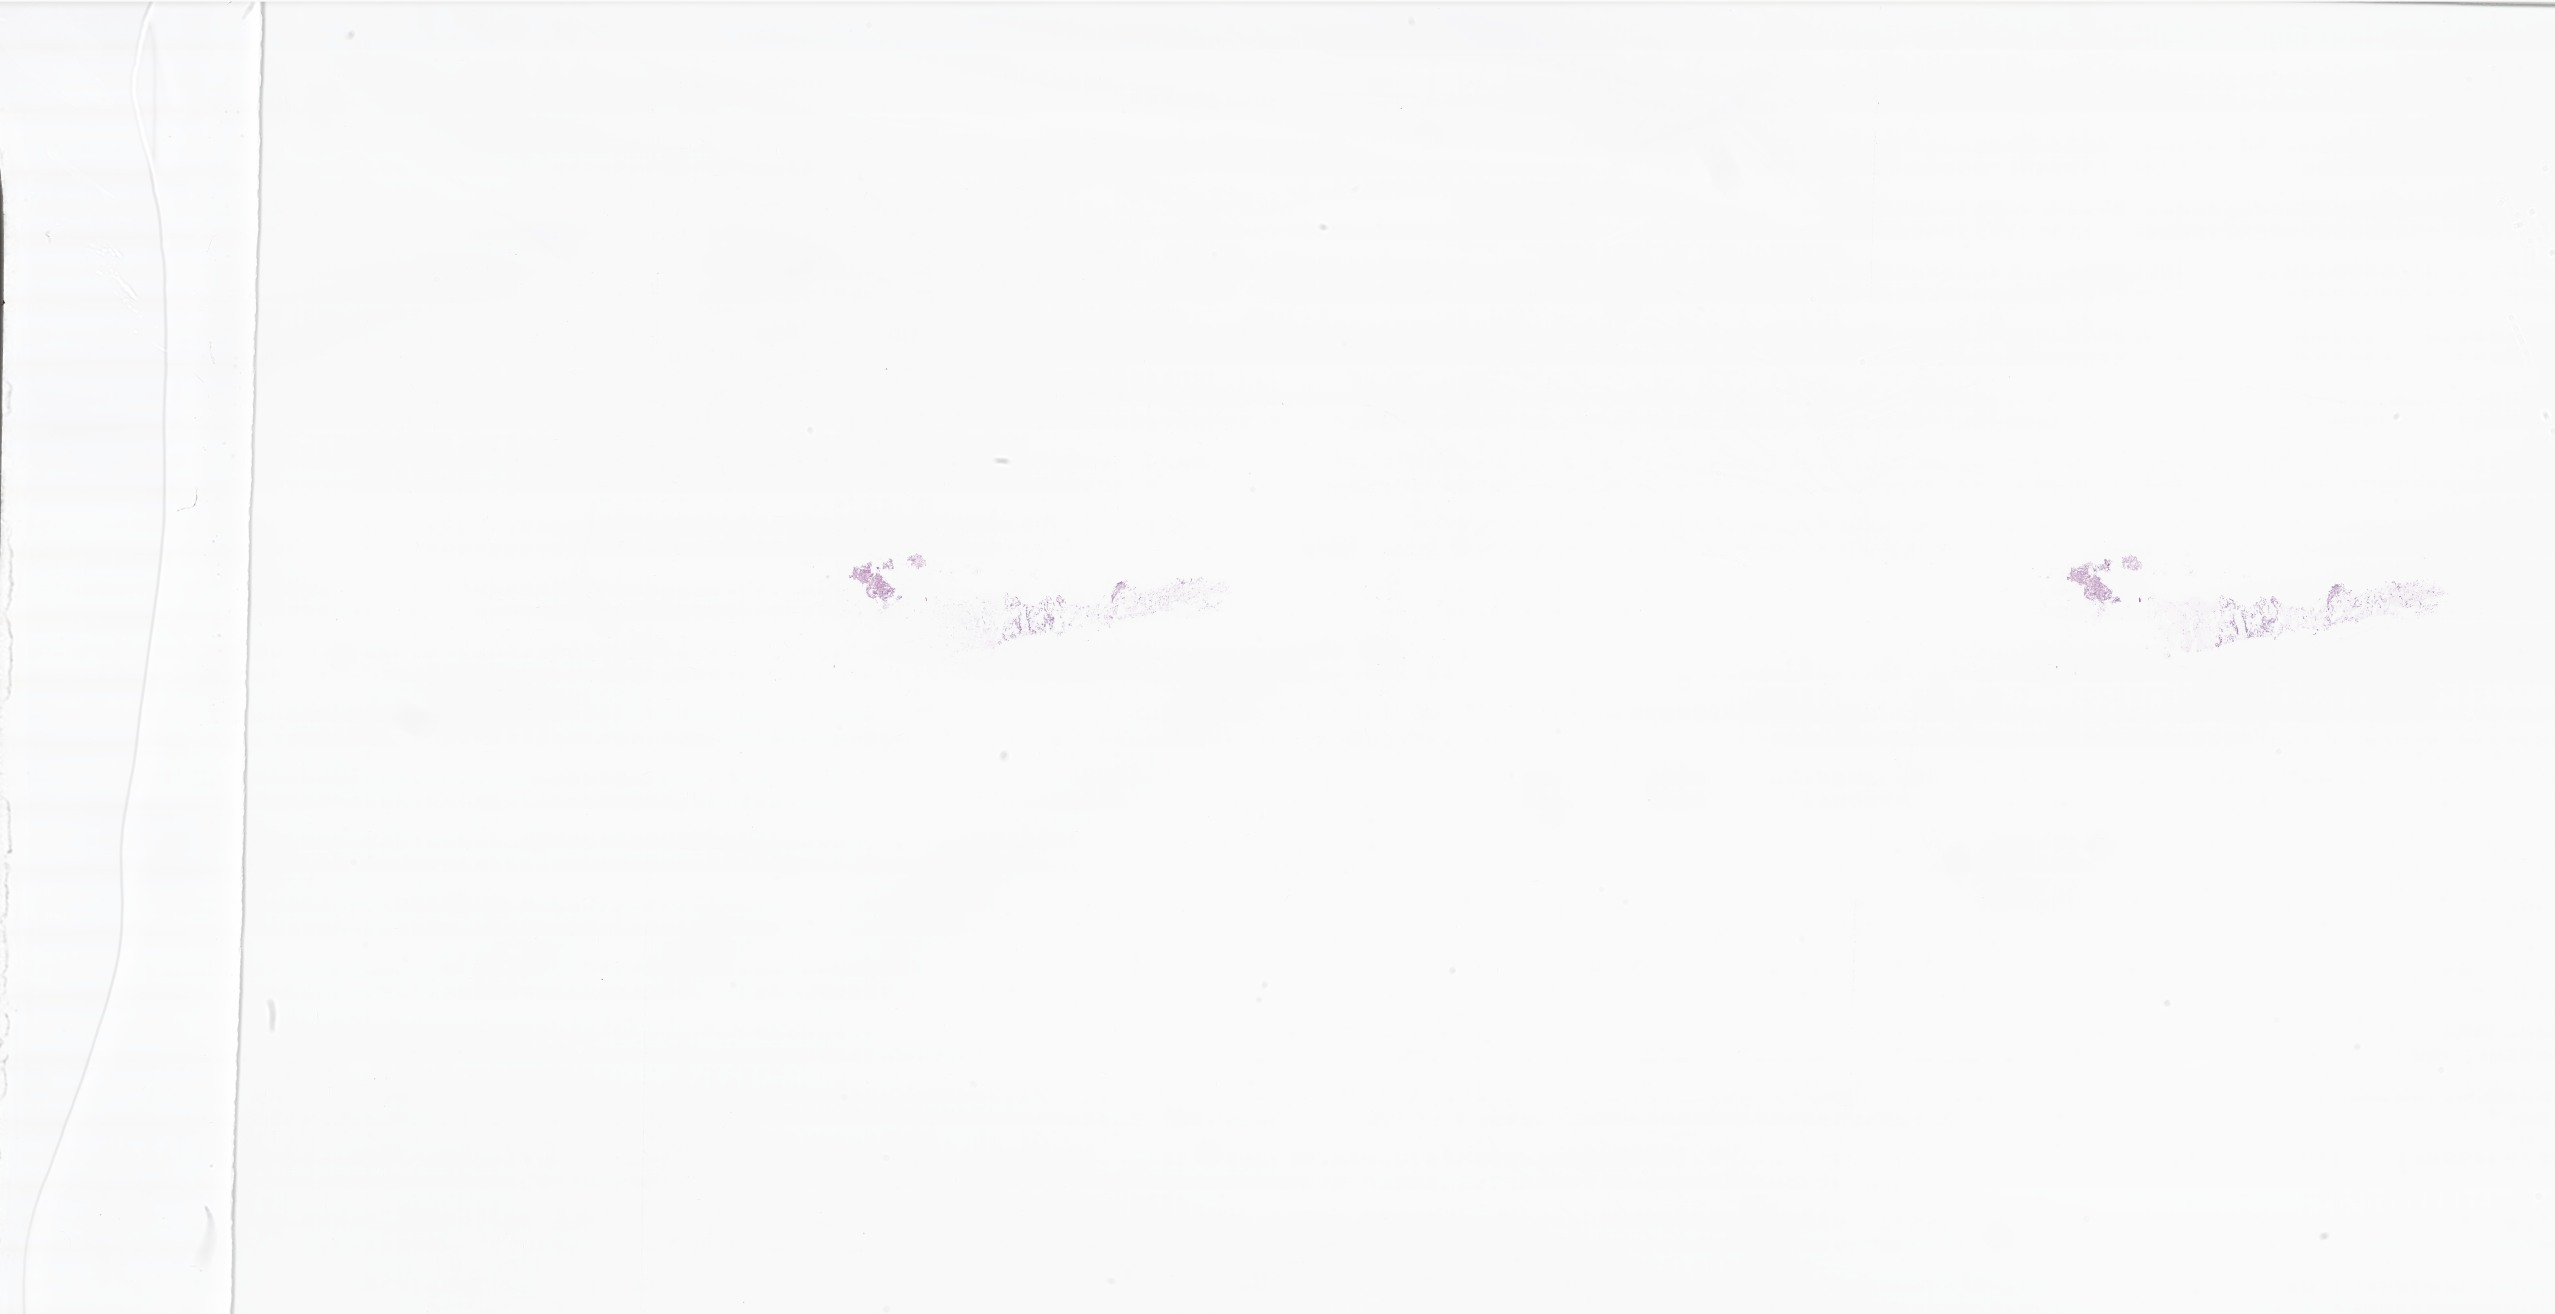
Whole-slide image, H&E stain, shown as a low-resolution overview of the whole scanned area (about 43.1 x 22.2 mm), frozen section, specimen: primary tumor, site: head of pancreas. Female patient; age at initial diagnosis 63 years. Pathologist review of this section (percent, as recorded): tumor cells 70%, tumor nuclei 70%, stromal cells 30%, necrosis 0%, normal cells 0%. Infiltration values recorded for this section: lymphocyte infiltration 4%, monocyte infiltration 2%, neutrophil infiltration 6%.
Histologic diagnosis: Infiltrating duct carcinoma, NOS.